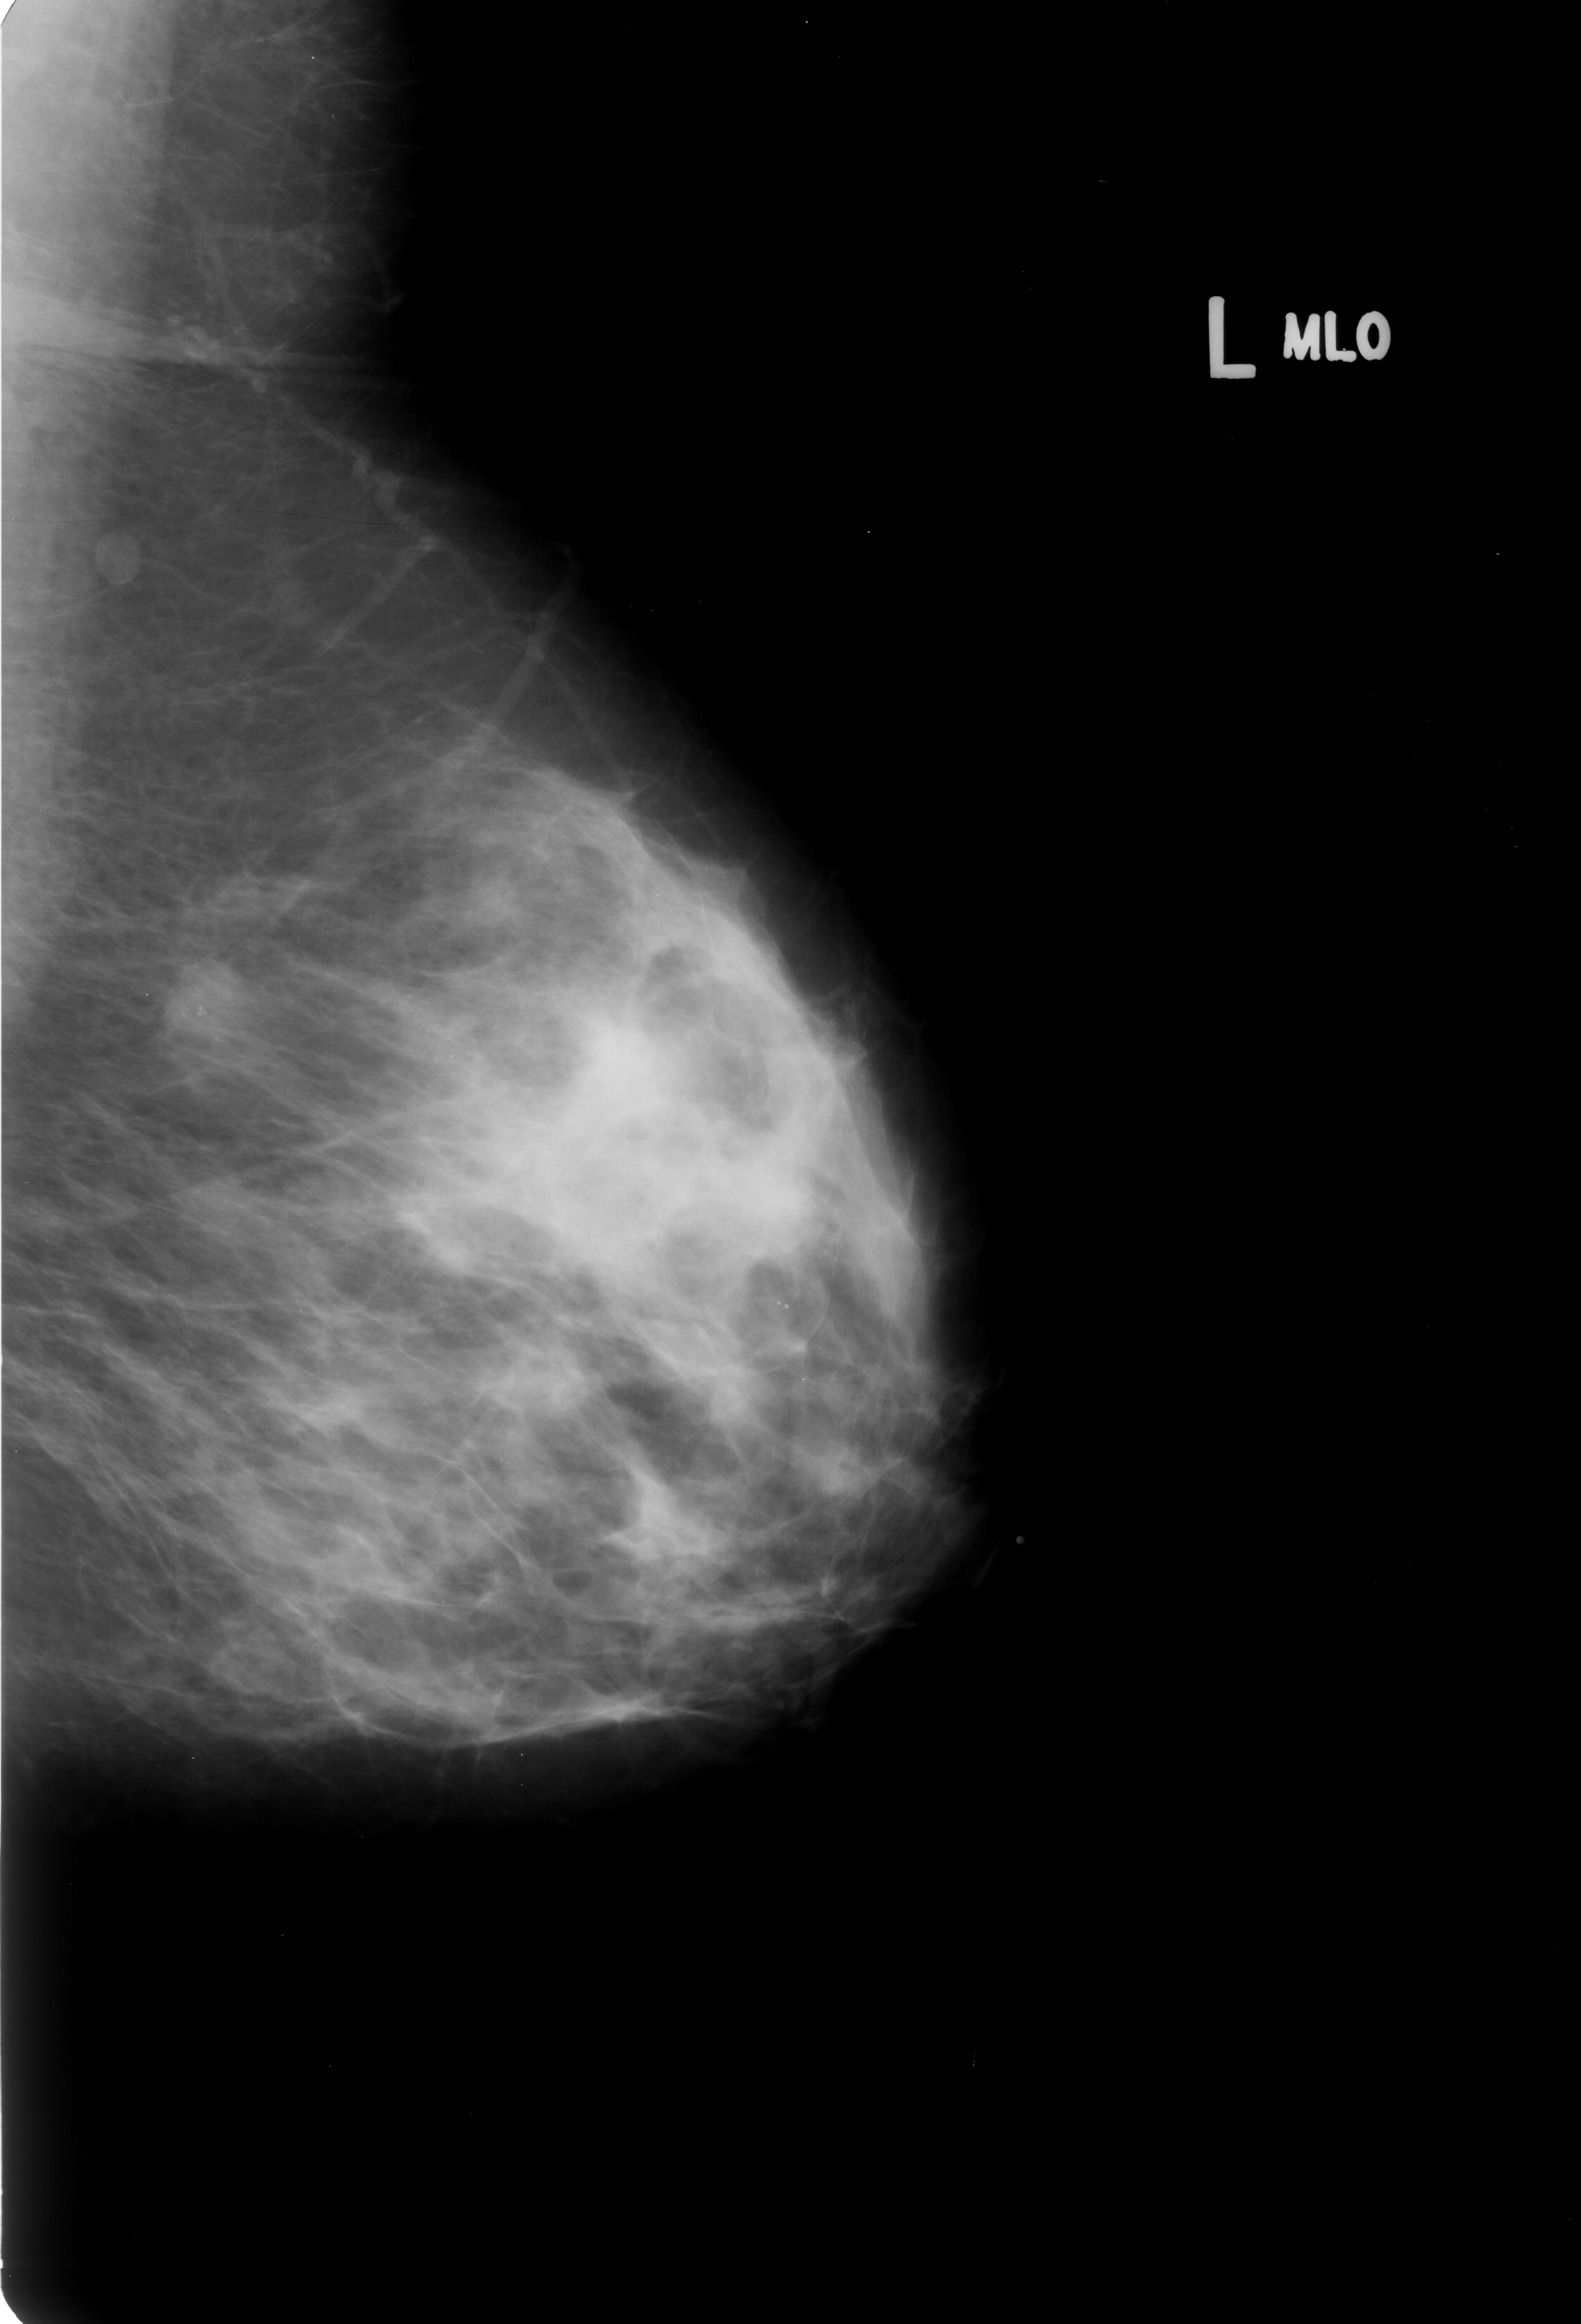
Digitized screen-film mammogram; left breast; MLO view; breast composition: heterogeneously dense (BI-RADS density category 3 of 4).
- Radiologist-marked abnormalities on this image: Finding 1 of 2: calcifications, morphology punctate, distribution segmental; BI-RADS assessment category 4; subtlety rating 3 on a 1 (subtle) to 5 (obvious) scale; pathology (as recorded): benign.
- Finding 2 of 2: calcifications, morphology punctate, distribution segmental; BI-RADS assessment category 4; pathology (as recorded): benign.